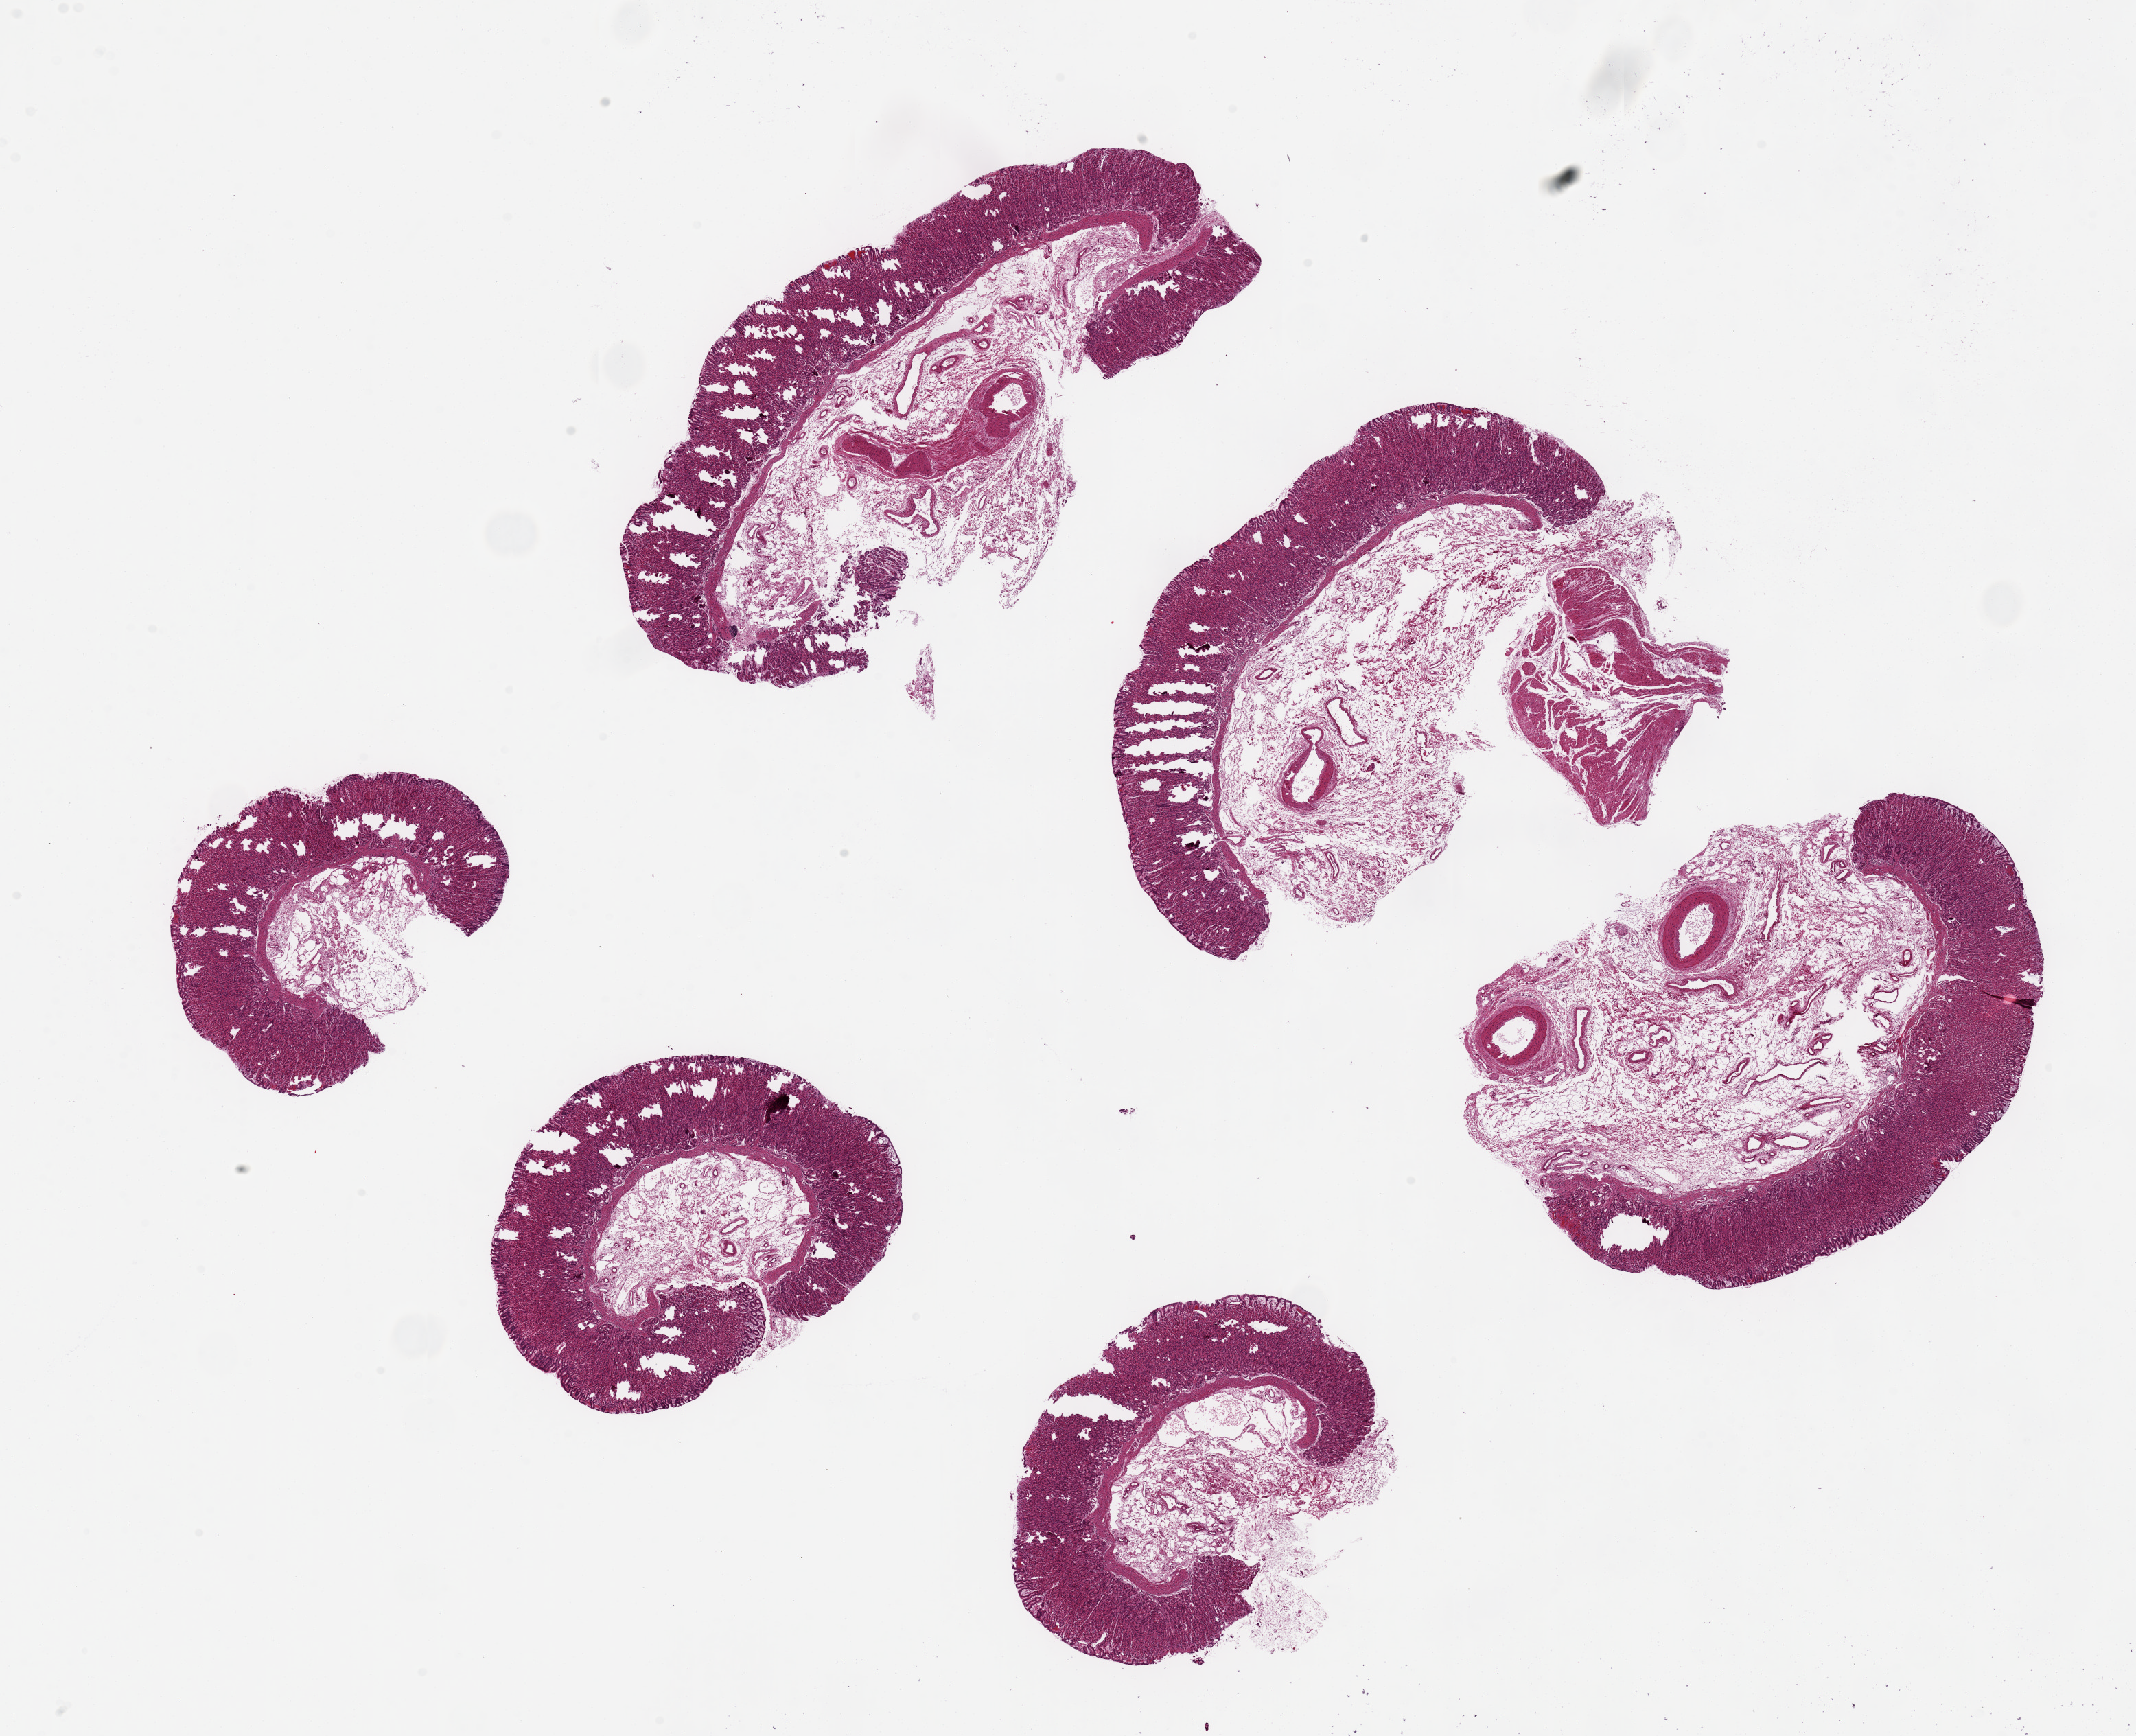
Whole-slide image, H&E stain — low-resolution overview of the scanned area, about 24.6 x 20.0 mm (acquisition: 20x scan), PAXgene-fixed, paraffin-embedded tissue, target tissue: stomach, donor tissue sample. Male donor.
Reviewer comment on this tissue sample: 6 pieces up to 8x4.5 mm; good mucosa; many mucosal tissue tears in every piece, doesn???t appear to be poor fixation.